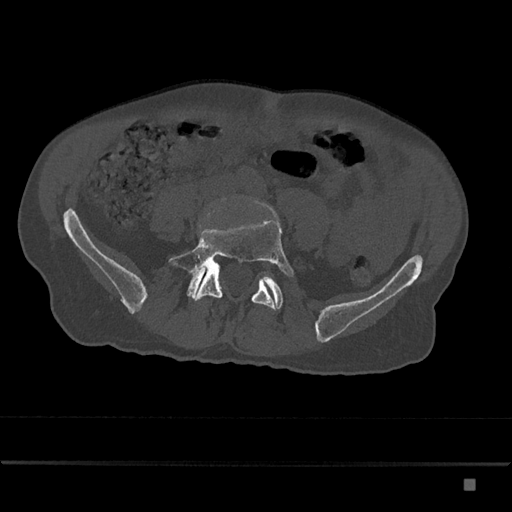
CT including the spine, one axial slice; slice 277 of 797 in the series (ordered by position); 120 kVp; bone window (W 1800 / L 400 HU); 0.5 mm slice thickness; 512 × 512 image matrix. Patient: male, 72 years. Case-level facts recorded for this patient, not image findings: primary cancer: prostate.
Annotated regions visible in this slice (semi-automatic segmentation, software-assisted and operator-edited):
- L5 vertebra: bounding box (x1, y1, x2, y2) in pixels: (168, 203, 294, 310)